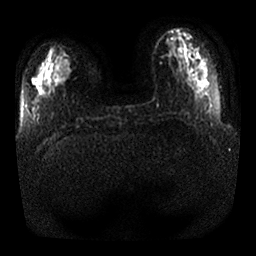
Breast MRI, one axial slice. Slice 8 of 25 in the series (ordered by position). Diffusion-weighted series; image 2 of 4 stored at this slice position (different b-values; order by instance number). 1.5 T. 4 mm slice thickness. 256 × 256 image matrix. Female patient.
Structures marked on this image (manually delineated by an expert):
- tumour on diffusion-weighted imaging: bounding box [x1, y1, x2, y2] px = [54, 53, 71, 80]